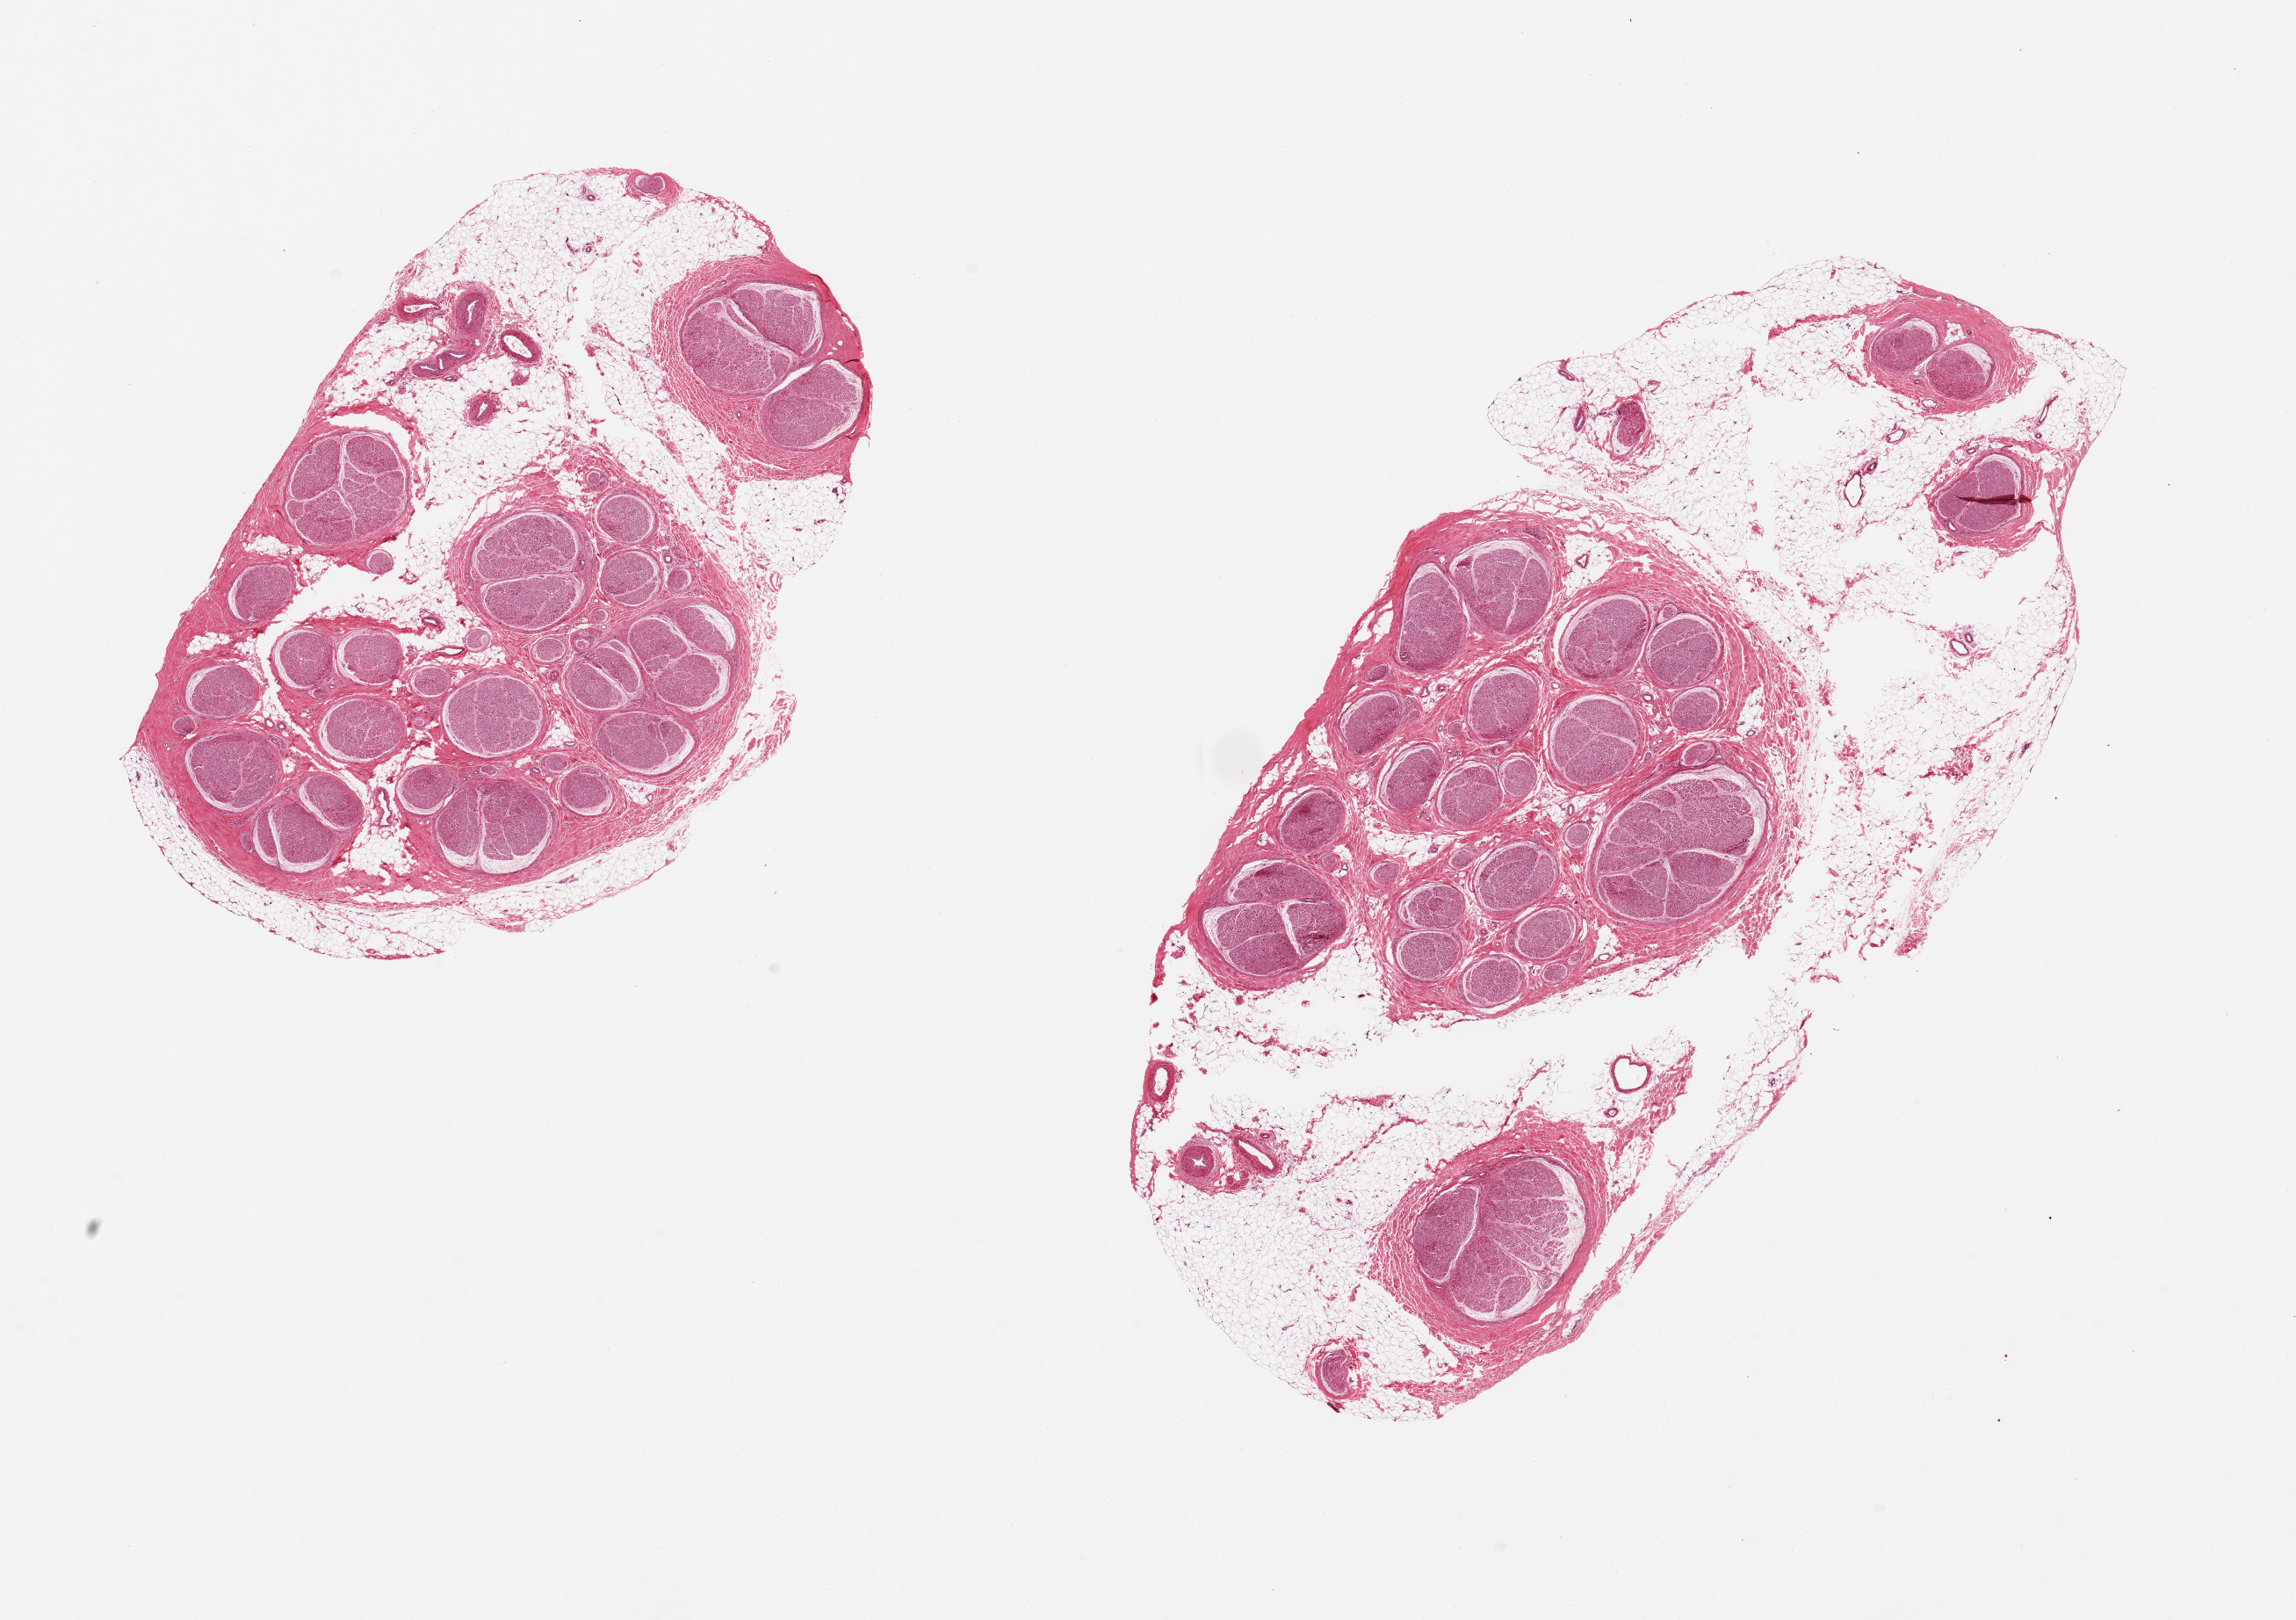
Digitized haematoxylin and eosin-stained section — shown as a low-resolution overview of the whole scanned area (about 20.7 x 14.6 mm, from a 20x scan), PAXgene-fixed paraffin-embedded (PFPE) section, sampled site (target tissue): tibial nerve, tissue donor sample. Donor: male.
Reviewer comment on this tissue sample: 2 pieces ~5mm. Note: One with extensive adherent fat up to 4-5mm thick with commingling smaller nerve twigs.